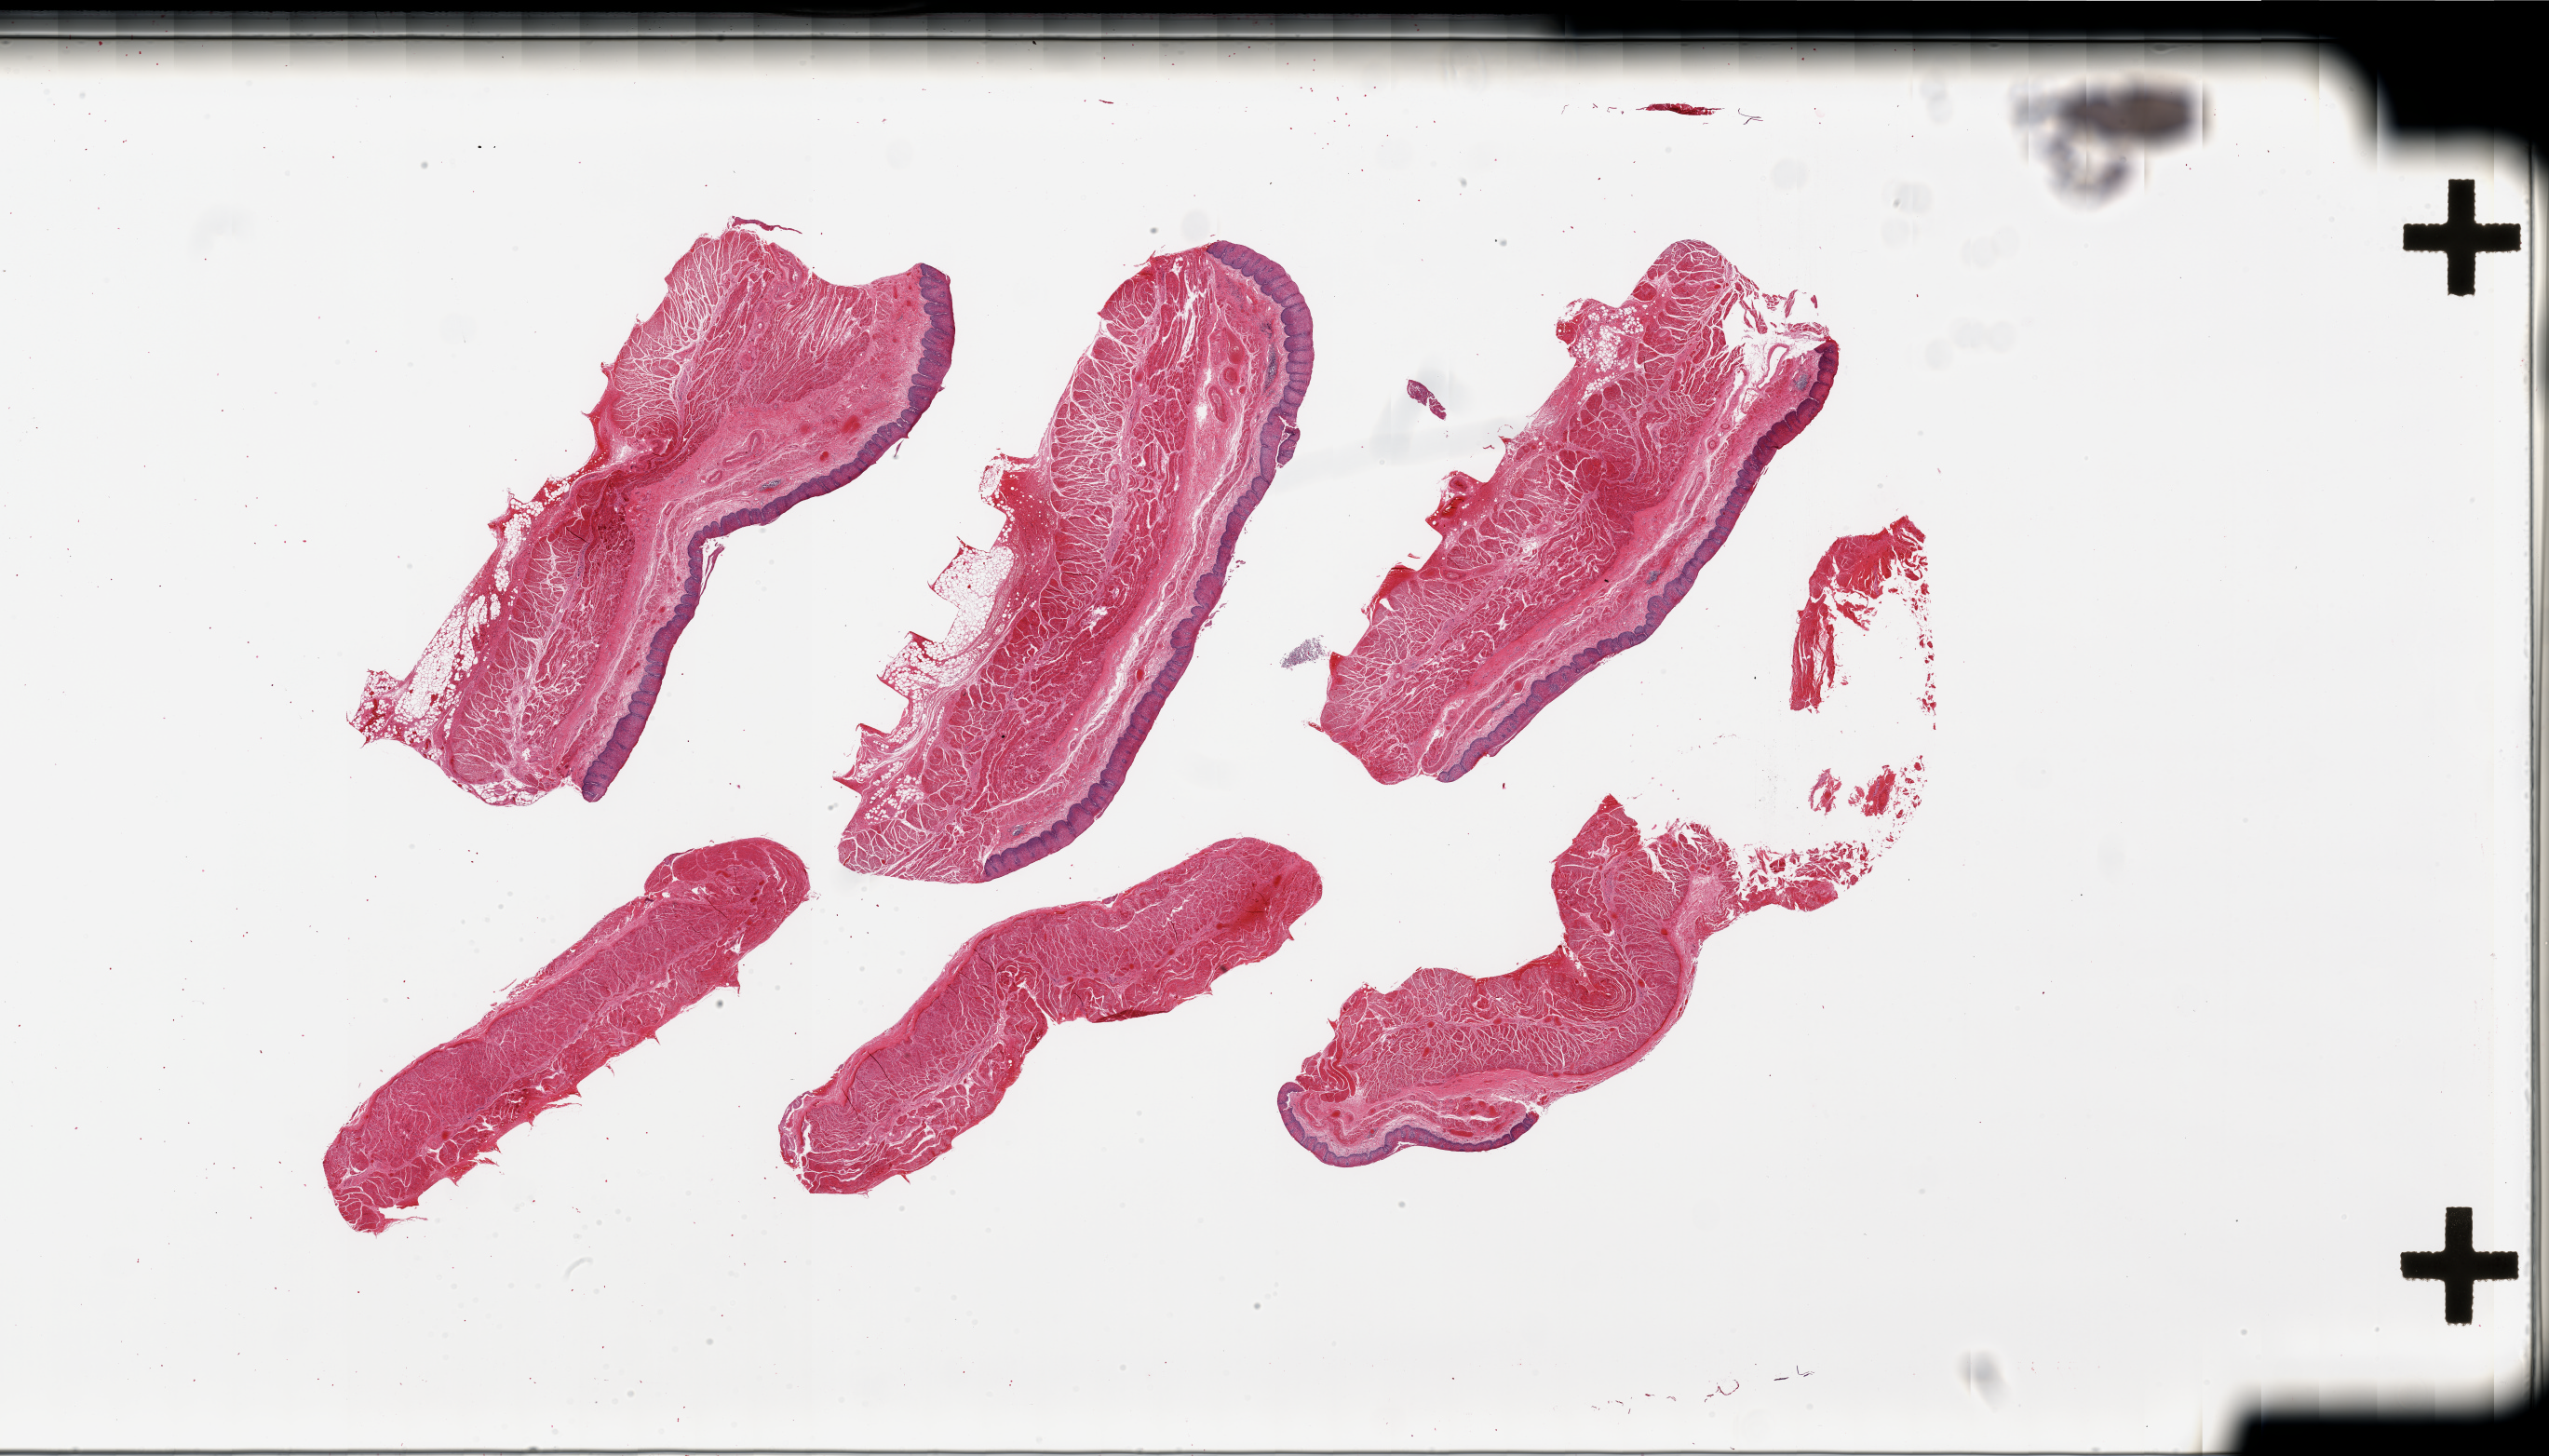
Digitized haematoxylin and eosin-stained section, whole scanned area (about 43.3 x 24.7 mm, slide scanned at 20x) shown as a low-resolution overview; PAXgene-fixed paraffin-embedded (PFPE) section; sampled site (target tissue): gastroesophageal junction; tissue donor sample. Male donor.
Review note (as recorded): 6 pieces, mucosa, not target muscularis.